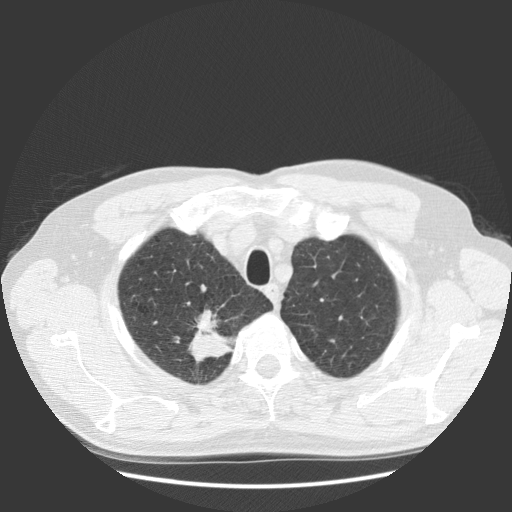
Low-dose screening chest CT, one axial slice. Position 109 of 131 along the scan axis. 140 kVp. Lung window (W 1500 / L -600 HU). 2.5 mm slice thickness. 512 × 512 image matrix, field of view 369 × 369 mm.
Outlined on this slice (outlined manually by an expert reader):
- lesion 1 (tumor, upper lobe of right lung): bounding box (x1, y1, x2, y2) in pixels: (188, 310, 236, 363)